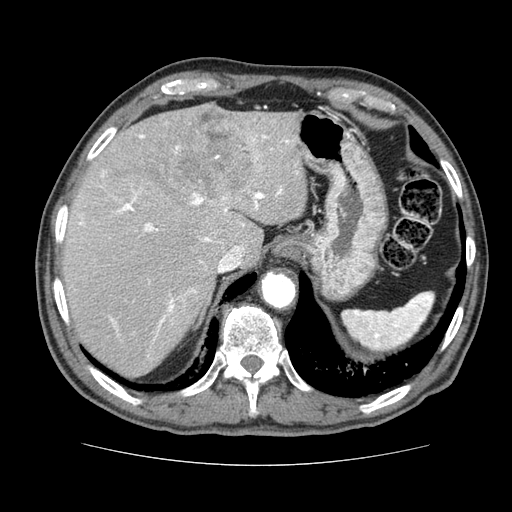
Contrast-enhanced abdominal CT (liver protocol), one axial slice; slice 56 of 79 in the series (ordered by position); 120 kVp; soft-tissue window (W 400 / L 40 HU); 512 × 512 image matrix, field of view 360 × 360 mm. Case-level facts recorded for this patient, not image findings: diagnosis: hepatocellular carcinoma (patient treated with transarterial chemoembolisation; whether this scan precedes or follows treatment is not stated here); TNM stage (as recorded): Stage-I; Child-Pugh class: A; tumour nodularity: uninodular.
Outlined on this slice (semi-automatically segmented with operator editing):
- liver parenchyma outside the tumour (the mass and vessels are separate outlines, so this box may not span the whole liver): bounding box [x1, y1, x2, y2] px = [62, 104, 306, 377]
- mass: [143, 105, 264, 207]
- liver vessels: [78, 135, 298, 340]